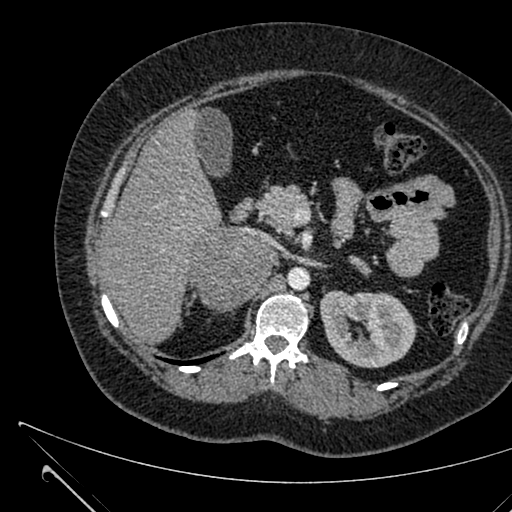
Contrast-enhanced abdominal CT, one axial slice; 120 kVp; intravenous contrast given; soft-tissue window (W 400 / L 40 HU); 512 × 512 image matrix, field of view 376 × 376 mm. Female patient, age 36 years. From the clinical record (not read from this slice): diagnosis: adrenocortical carcinoma; tumour side: right adrenal; tumour size at pathology: 10 cm; Ki-67 index: 20 %; stage (as recorded): 4.
Structures marked on this image (semi-automatically segmented with operator editing):
- mass: bounding box (x1, y1, x2, y2) in pixels: (192, 229, 274, 308)